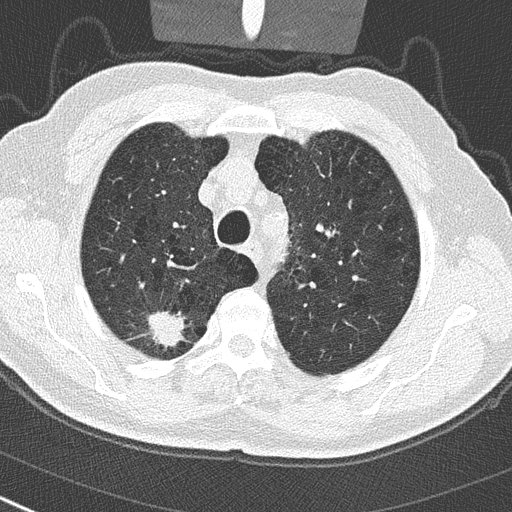
Low-dose screening chest CT, axial slice. First (baseline) screen. Lung window (W 1500 / L -600 HU). Lung (sharp) reconstruction kernel (B50f). Slice 61 of 290 in the series. Male participant, aged 65 years at enrolment.
- Expert reader's lesion annotation, box from (x=133, y=301) to (x=191, y=355) px.
- Reader record for this screening exam (exam-level; its link to the box is not recorded): non-calcified nodule or mass ≥4 mm, right upper lobe, 24 × 19 mm, spiculated (stellate) margins, soft tissue attenuation.
- Participant outcome: lung cancer diagnosed 32 days after this screen — non-small cell carcinoma, right upper lobe, poorly differentiated (G3), stage IA (AJCC 6th edition), 29 mm at pathology.